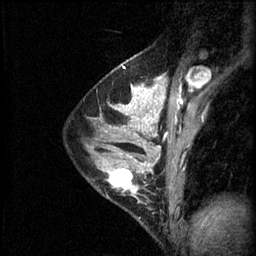
Breast MRI (dynamic contrast-enhanced), one sagittal slice. Position 37 of 60 along the scan axis. 3 images stored at this slice position (order not interpretable as contrast timing). 1.5 T. TE 4.2 ms, TR 11 ms. 2.1 mm slice thickness. 256 × 256 image matrix. Patient: female, 29 years.
Structures marked on this image (semi-automatically segmented with operator editing):
- analysis volume of interest (the breast-tissue region the enhancement analysis was run in; not a lesion): bounding box <95,164,153,225> (left, top, right, bottom; pixels)
- tumour enhancement mask (voxels above the 70 % enhancement threshold inside the analysis volume of interest): <107,166,153,193>